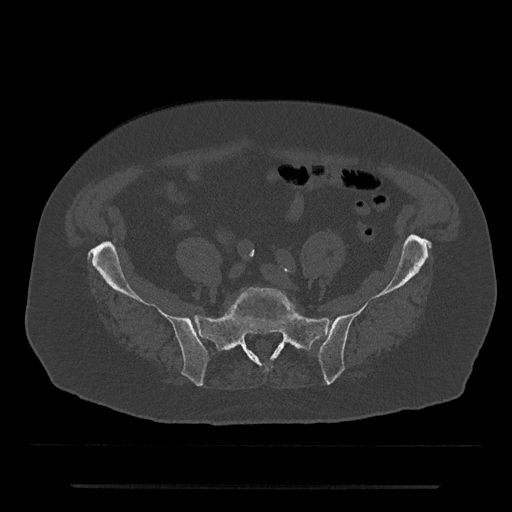
CT including the spine, one axial slice; slice 248 of 797 in the series (ordered by position); reconstruction kernel Br40s/3; bone window (W 1800 / L 400 HU); 512 × 512 image matrix, field of view 434 × 434 mm. Patient: male, 80 years. Case-level facts recorded for this patient, not image findings: primary cancer: prostate.
Structures marked on this image (semi-automatic segmentation, software-assisted and operator-edited):
- L5 vertebra: bounding box <227,287,298,318> (left, top, right, bottom; pixels)